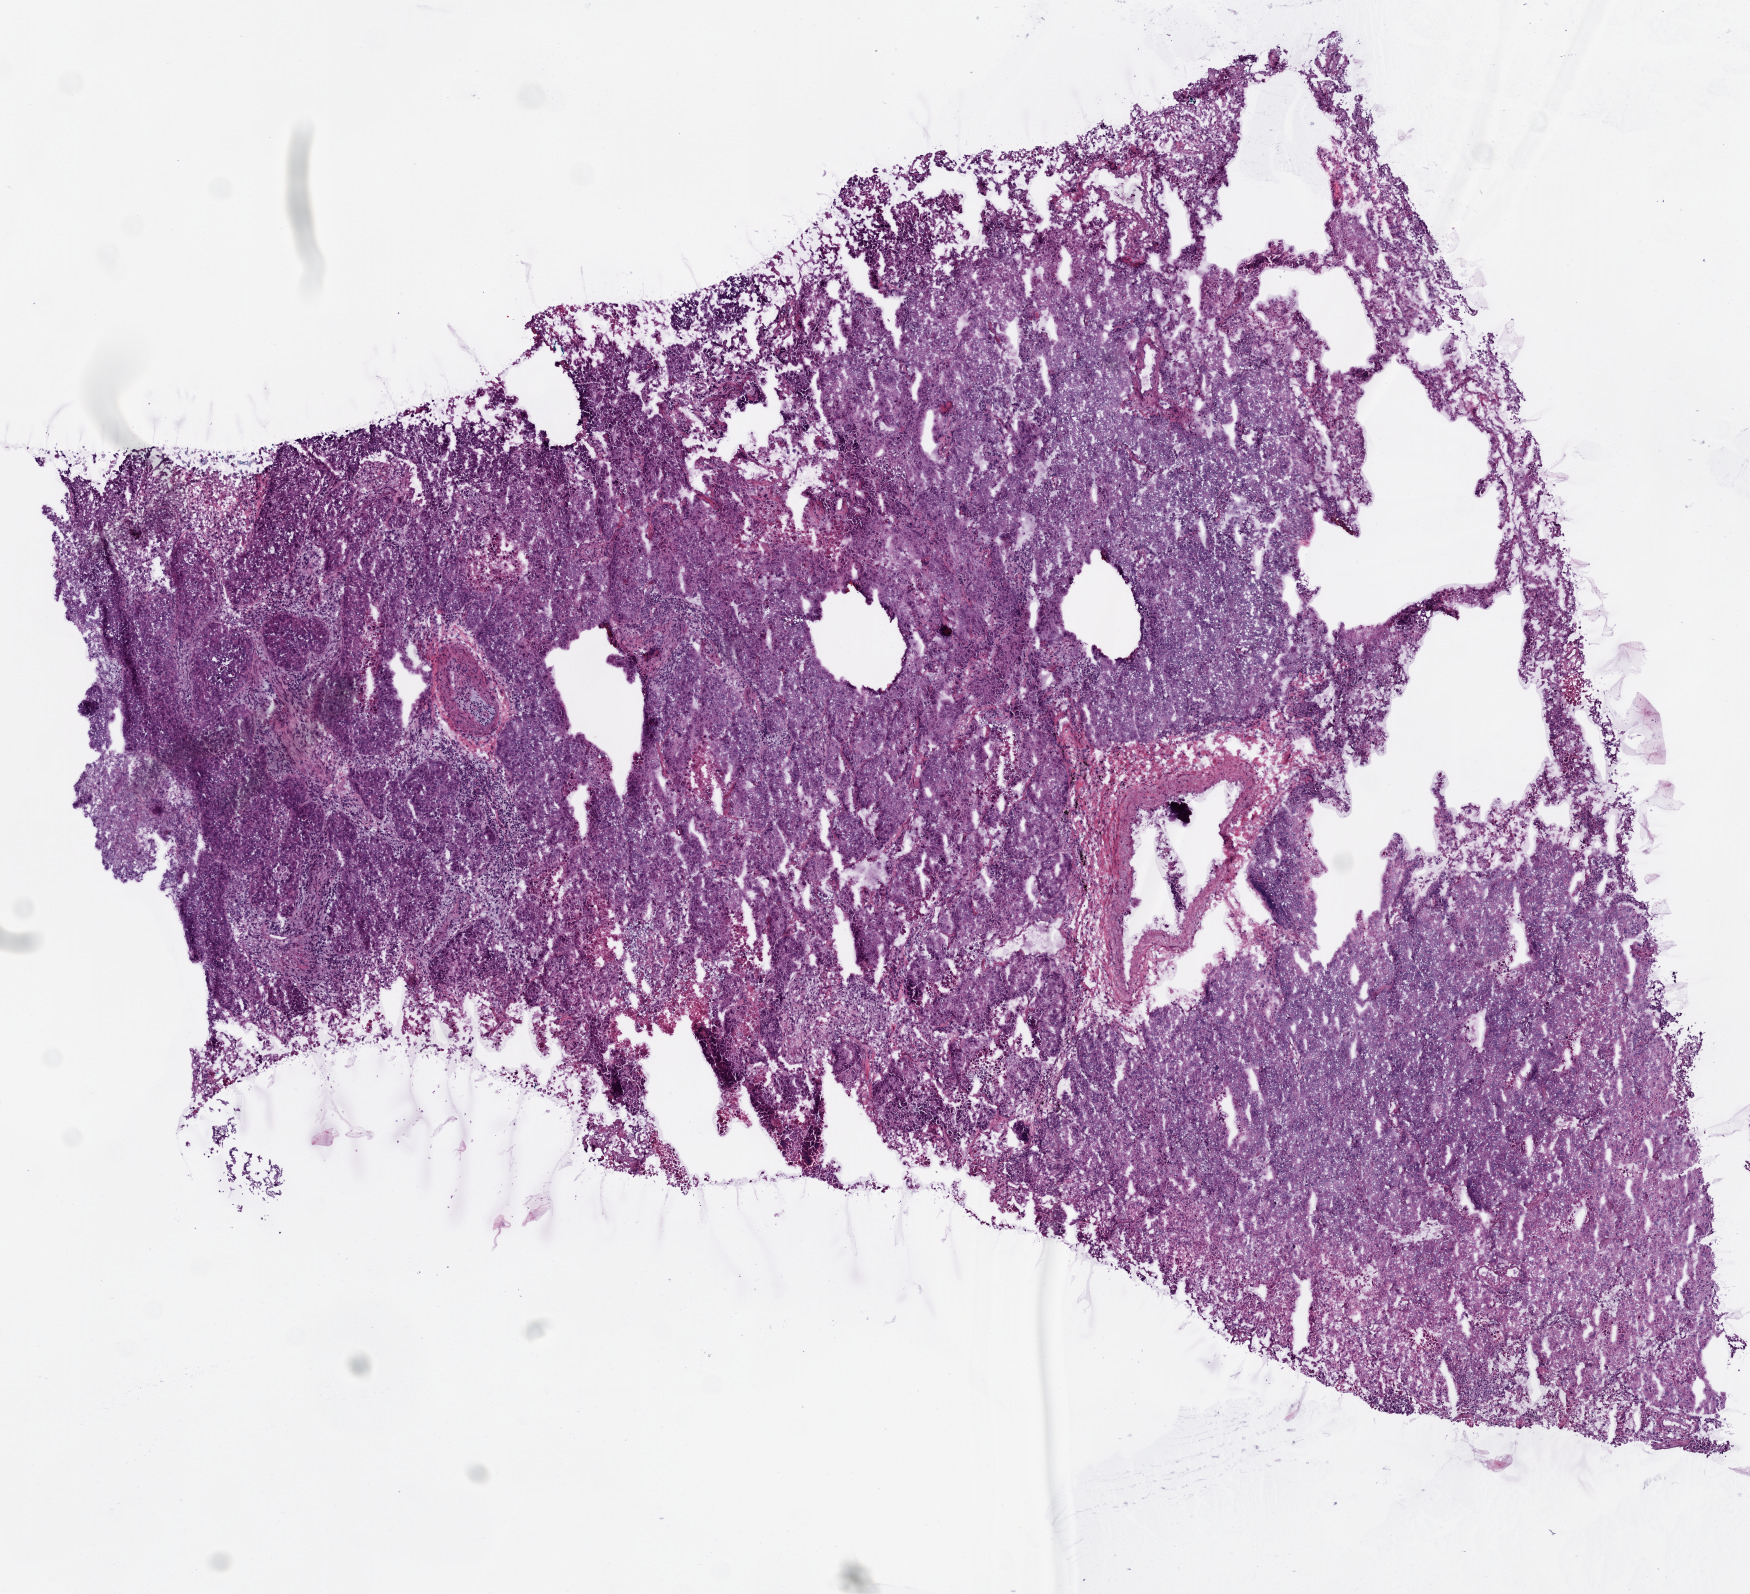
Whole-slide histology image, H&E-stained — low-resolution overview of the scanned area, about 7.0 x 6.4 mm (slide scanned at 20x), frozen section from the top of the tissue portion, lung, primary tumour sample. Male patient; age at initial diagnosis 80 years. Pathologist review of this section (percent, as recorded): tumour cells 90%, tumour nuclei 85%.
Diagnosis: Squamous cell carcinoma, NOS (lower lobe, lung).